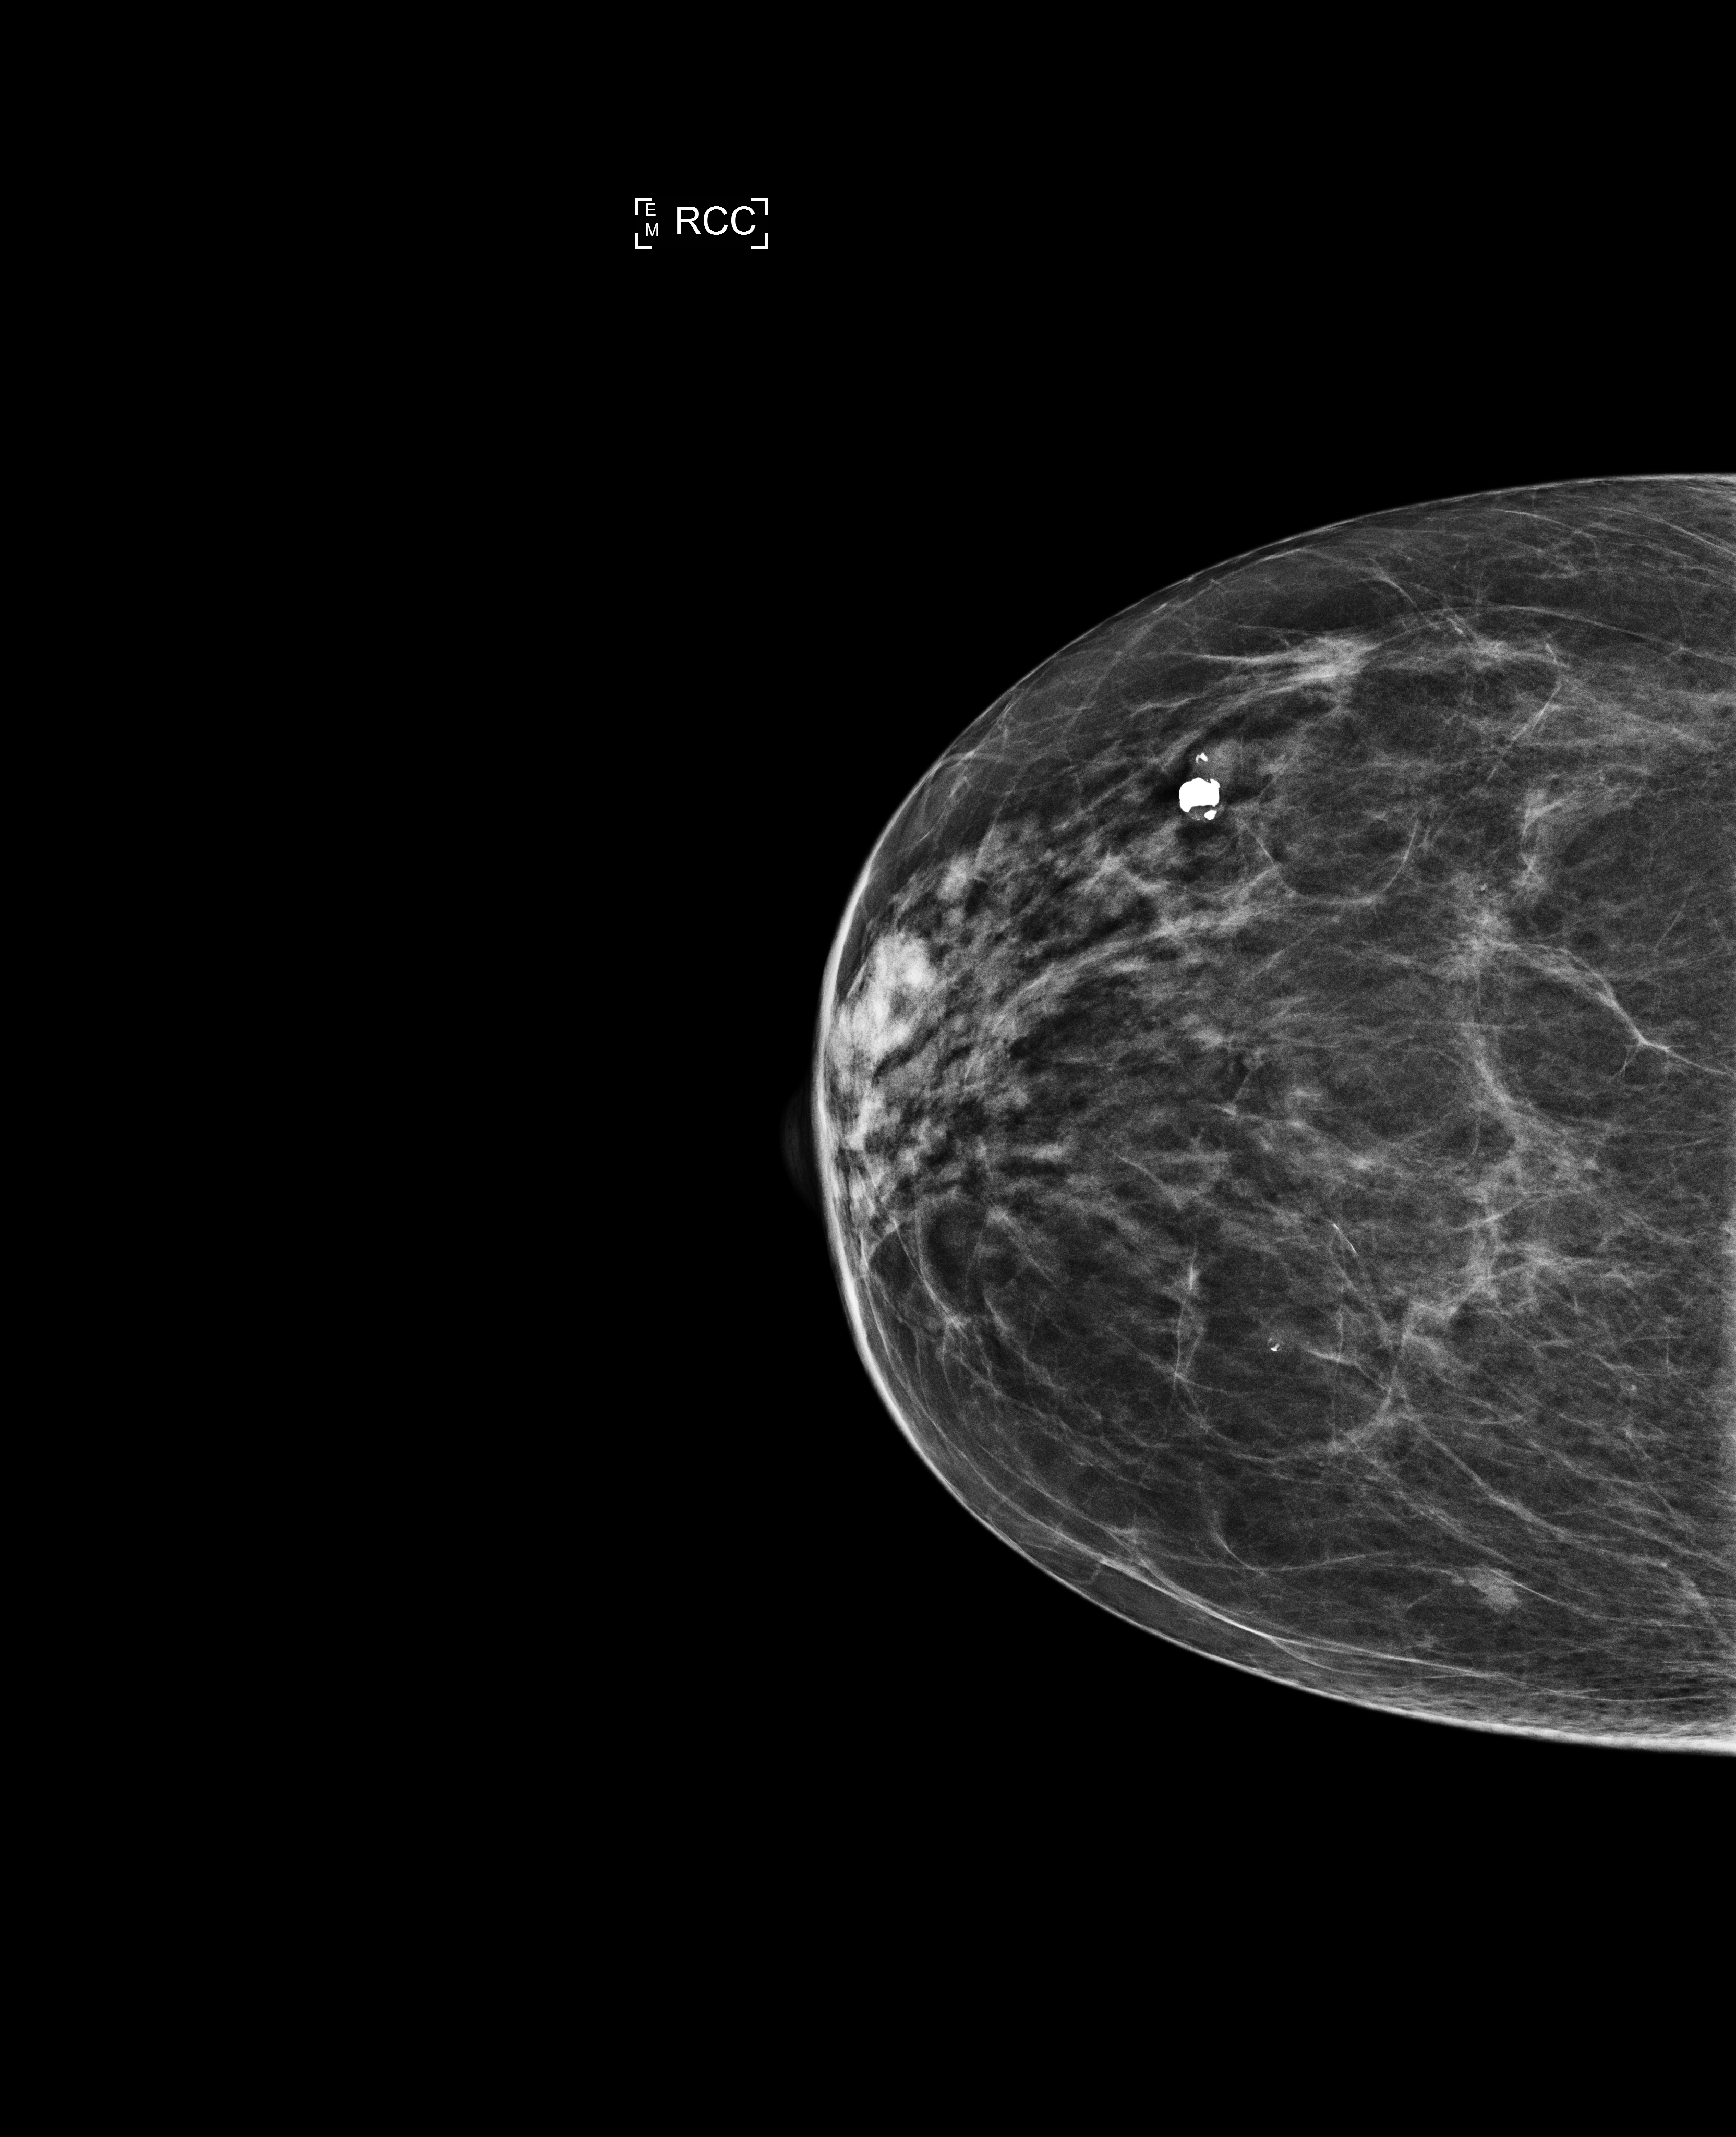
Screening examination; compressed breast thickness 40 mm; system: Selenia Dimensions. Patient: female, 65 years.
Image type: full-field digital mammogram. Breast: right. Projection: CC view.